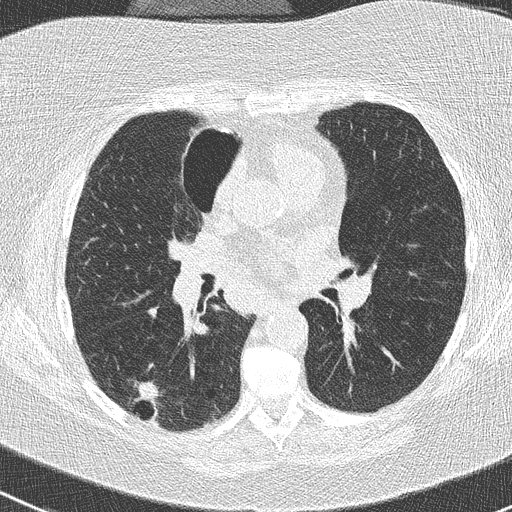
Axial slice from a low-dose chest CT screening exam; baseline screening round; lung window (W 1500 / L -600 HU); 2 mm slice thickness; lung (sharp) reconstruction kernel (B50f); 512 × 512 image matrix, field of view 310 × 310 mm. Female participant, aged 74 years at enrolment.
Expert reader's lesion annotation, bounding box [x1, y1, x2, y2] px = [120, 374, 174, 430]. The screening reader recorded 3 non-calcified nodules or masses ≥4 mm on this exam (right lower lobe, right upper lobe, left lower lobe); which of them this box marks is not recorded. Official screen result: positive, change unspecified: nodule(s) >= 4 mm or enlarging nodule(s), mass(es), or other non-specific abnormalities suspicious for lung cancer. Participant outcome: lung cancer diagnosed 16 days after this screen — non-small cell carcinoma, right lower lobe, poorly differentiated (G3), stage IIIA (AJCC 6th edition), 28 mm at pathology.